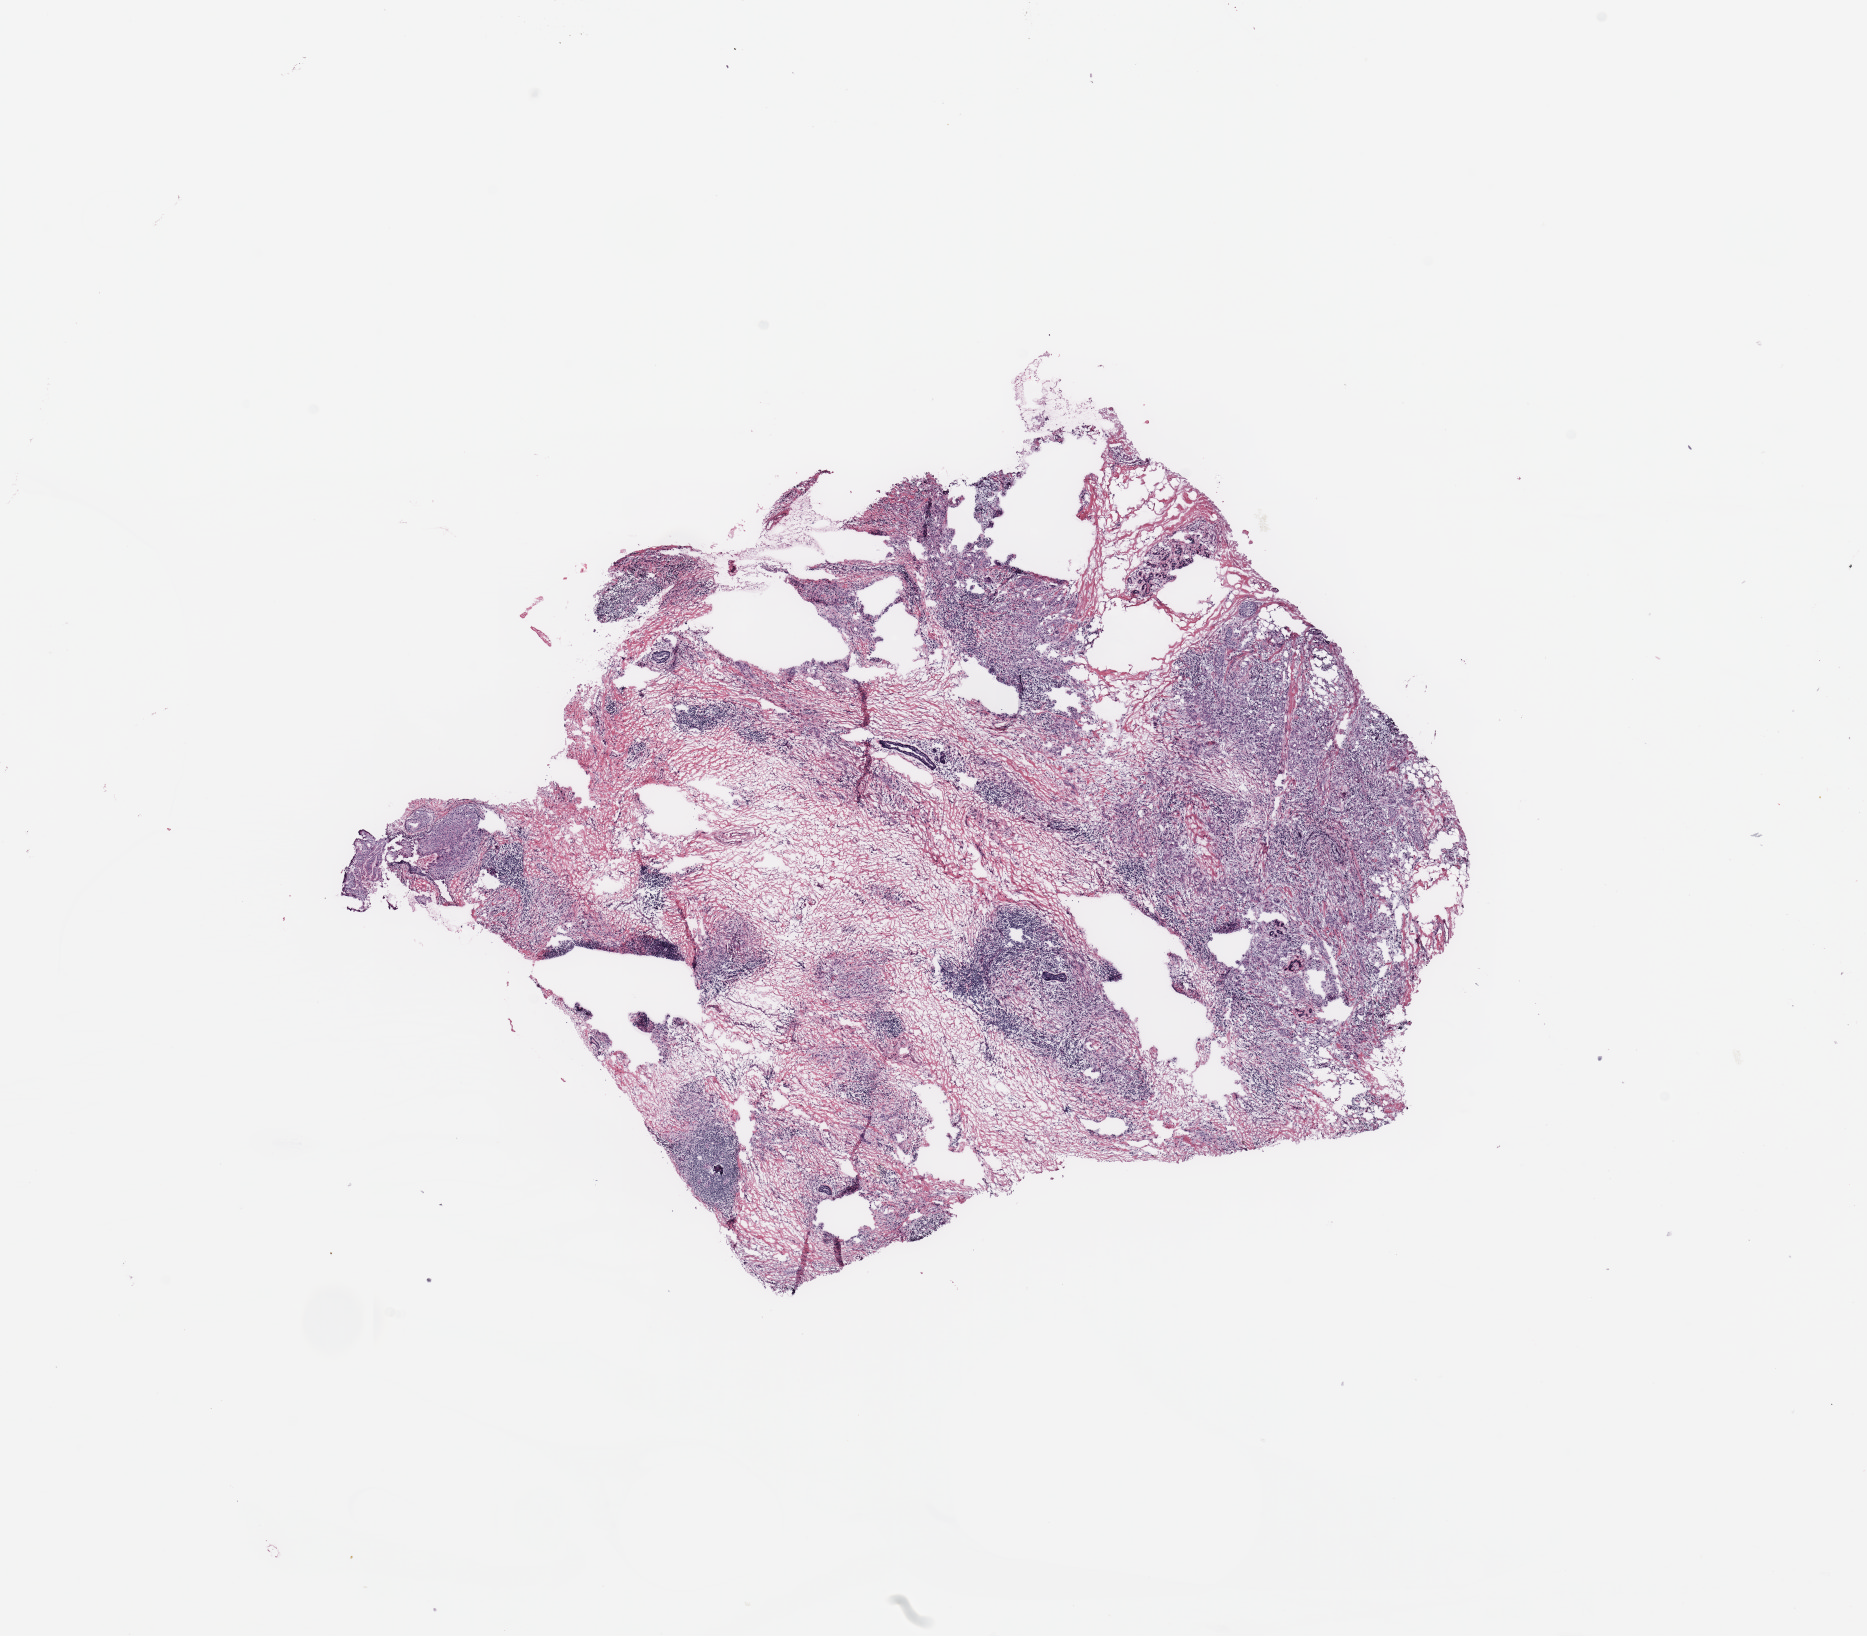
Digitized H&E-stained tissue section (whole slide), a low-resolution overview of the entire scanned area, about 14.8 x 12.9 mm (acquisition: 20x scan); breast, tissue type not recorded.
• patient diagnosis (cohort enrolment): breast cancer (breast)